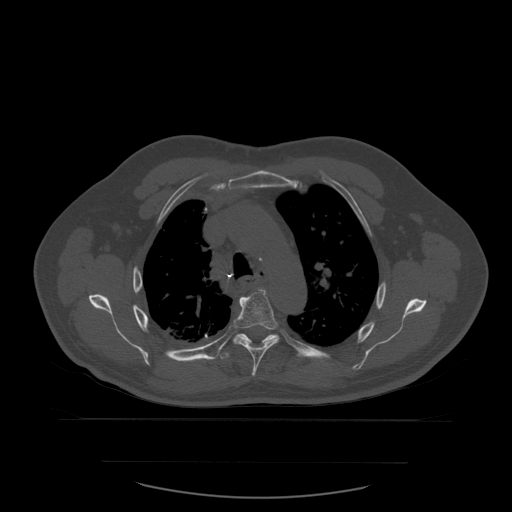
CT including the spine, one axial slice. Bone window (W 1800 / L 400 HU). 1.25 mm slice thickness. 512 × 512 image matrix, field of view 479 × 479 mm. Patient age 71 years. Case-level facts recorded for this patient, not image findings: primary cancer: lung.
Structures marked on this image (semi-automatic segmentation, software-assisted and operator-edited):
- T5 vertebra: bounding box (x1, y1, x2, y2) in pixels: (233, 289, 280, 377)
- T6 vertebra: (222, 334, 278, 359)